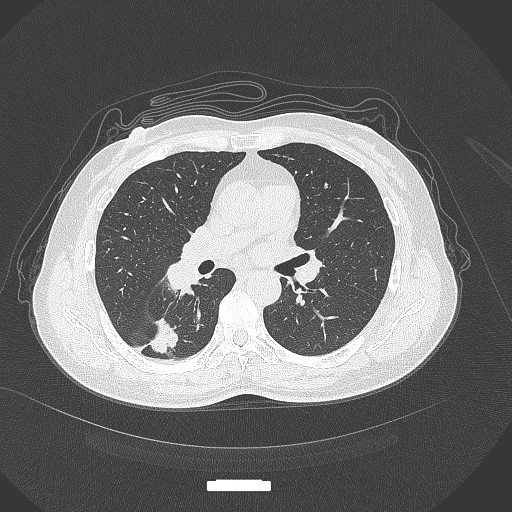
Chest CT, one axial slice. Position 169 of 352 along the scan axis. Reconstruction kernel B70f. 120 kVp. Lung window (W 1500 / L -600 HU). 1 mm slice thickness. 512 × 512 image matrix, field of view 400 × 400 mm. Female patient, age 55 years. Case-level facts recorded for this patient, not image findings: clinical TNM (as recorded): T1c N1 M0.
Annotated regions visible in this slice (rectangle marked by the reading radiologist):
- lung tumour (recorded histology: adenocarcinoma): box from (x=147, y=314) to (x=181, y=355) px